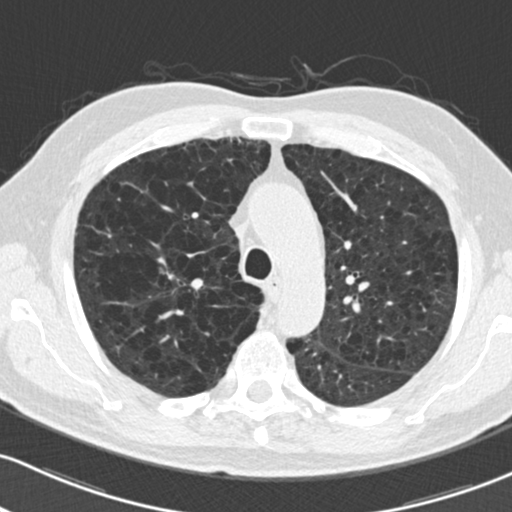
Axial slice from a low-dose chest CT screening exam; second screening round (one year after baseline); lung window (W 1500 / L -600 HU); 2 mm slice thickness; standard (soft-tissue) reconstruction kernel (B30f); 120 kVp; slice 55 of 204 in the series. Male participant, aged 73 years at enrolment. Current smoker at enrolment.
Lesion marked by an expert reader, bounding box [x1, y1, x2, y2] px = [147, 258, 200, 293]. The exam's reader record, not a measurement of the box and not confirmed to be the same lesion: non-calcified nodule or mass ≥4 mm, right upper lobe, 10 × 9 mm, smooth margins, soft tissue attenuation, pre-existing on the prior screen: yes; interval growth: yes. Official screen result: positive, other. Lung cancer was diagnosed 51 days after this screen: squamous cell carcinoma, NOS, right upper lobe, stage IA (AJCC 6th edition), 10 mm at pathology.